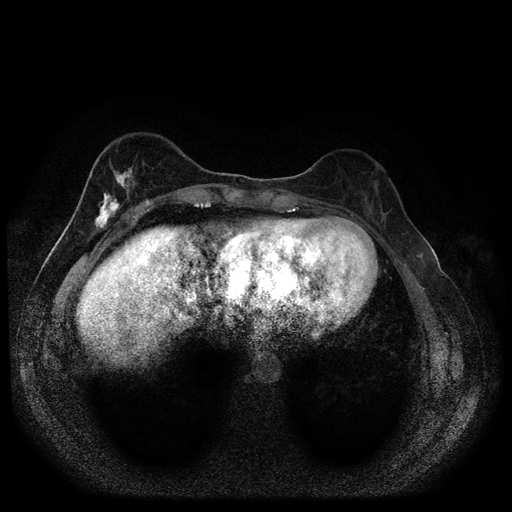
Breast MRI (dynamic contrast-enhanced, multi-phase), one axial slice; slice 33 of 116 in the series (ordered by position); dynamic contrast-enhanced series, time point 2 of 5 at this slice position (early post-contrast); 1.5 T; TE 2.7 ms, TR 5.4 ms; 512 × 512 image matrix, field of view 330 × 330 mm. Female patient, age 49 years.
Annotated regions visible in this slice (semi-automatic segmentation, software-assisted and operator-edited):
- breast lesion (labelled 'tumour' in the annotation; benign lesions carry a separate 'benign' label): box from (x=90, y=164) to (x=135, y=233) px